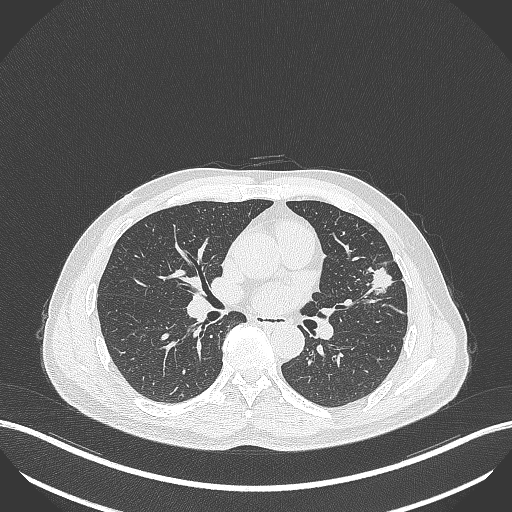
Chest CT, one axial slice. Position 208 of 418 along the scan axis. Lung window (W 1500 / L -600 HU). 1 mm slice thickness. 512 × 512 image matrix, field of view 400 × 400 mm. Male patient, age 55 years. Case-level facts recorded for this patient, not image findings: clinical TNM (as recorded): T1c N0 M0.
Structures marked on this image (rectangle marked by the reading radiologist):
- lung tumour (recorded histology: adenocarcinoma): box from (x=362, y=264) to (x=394, y=299) px